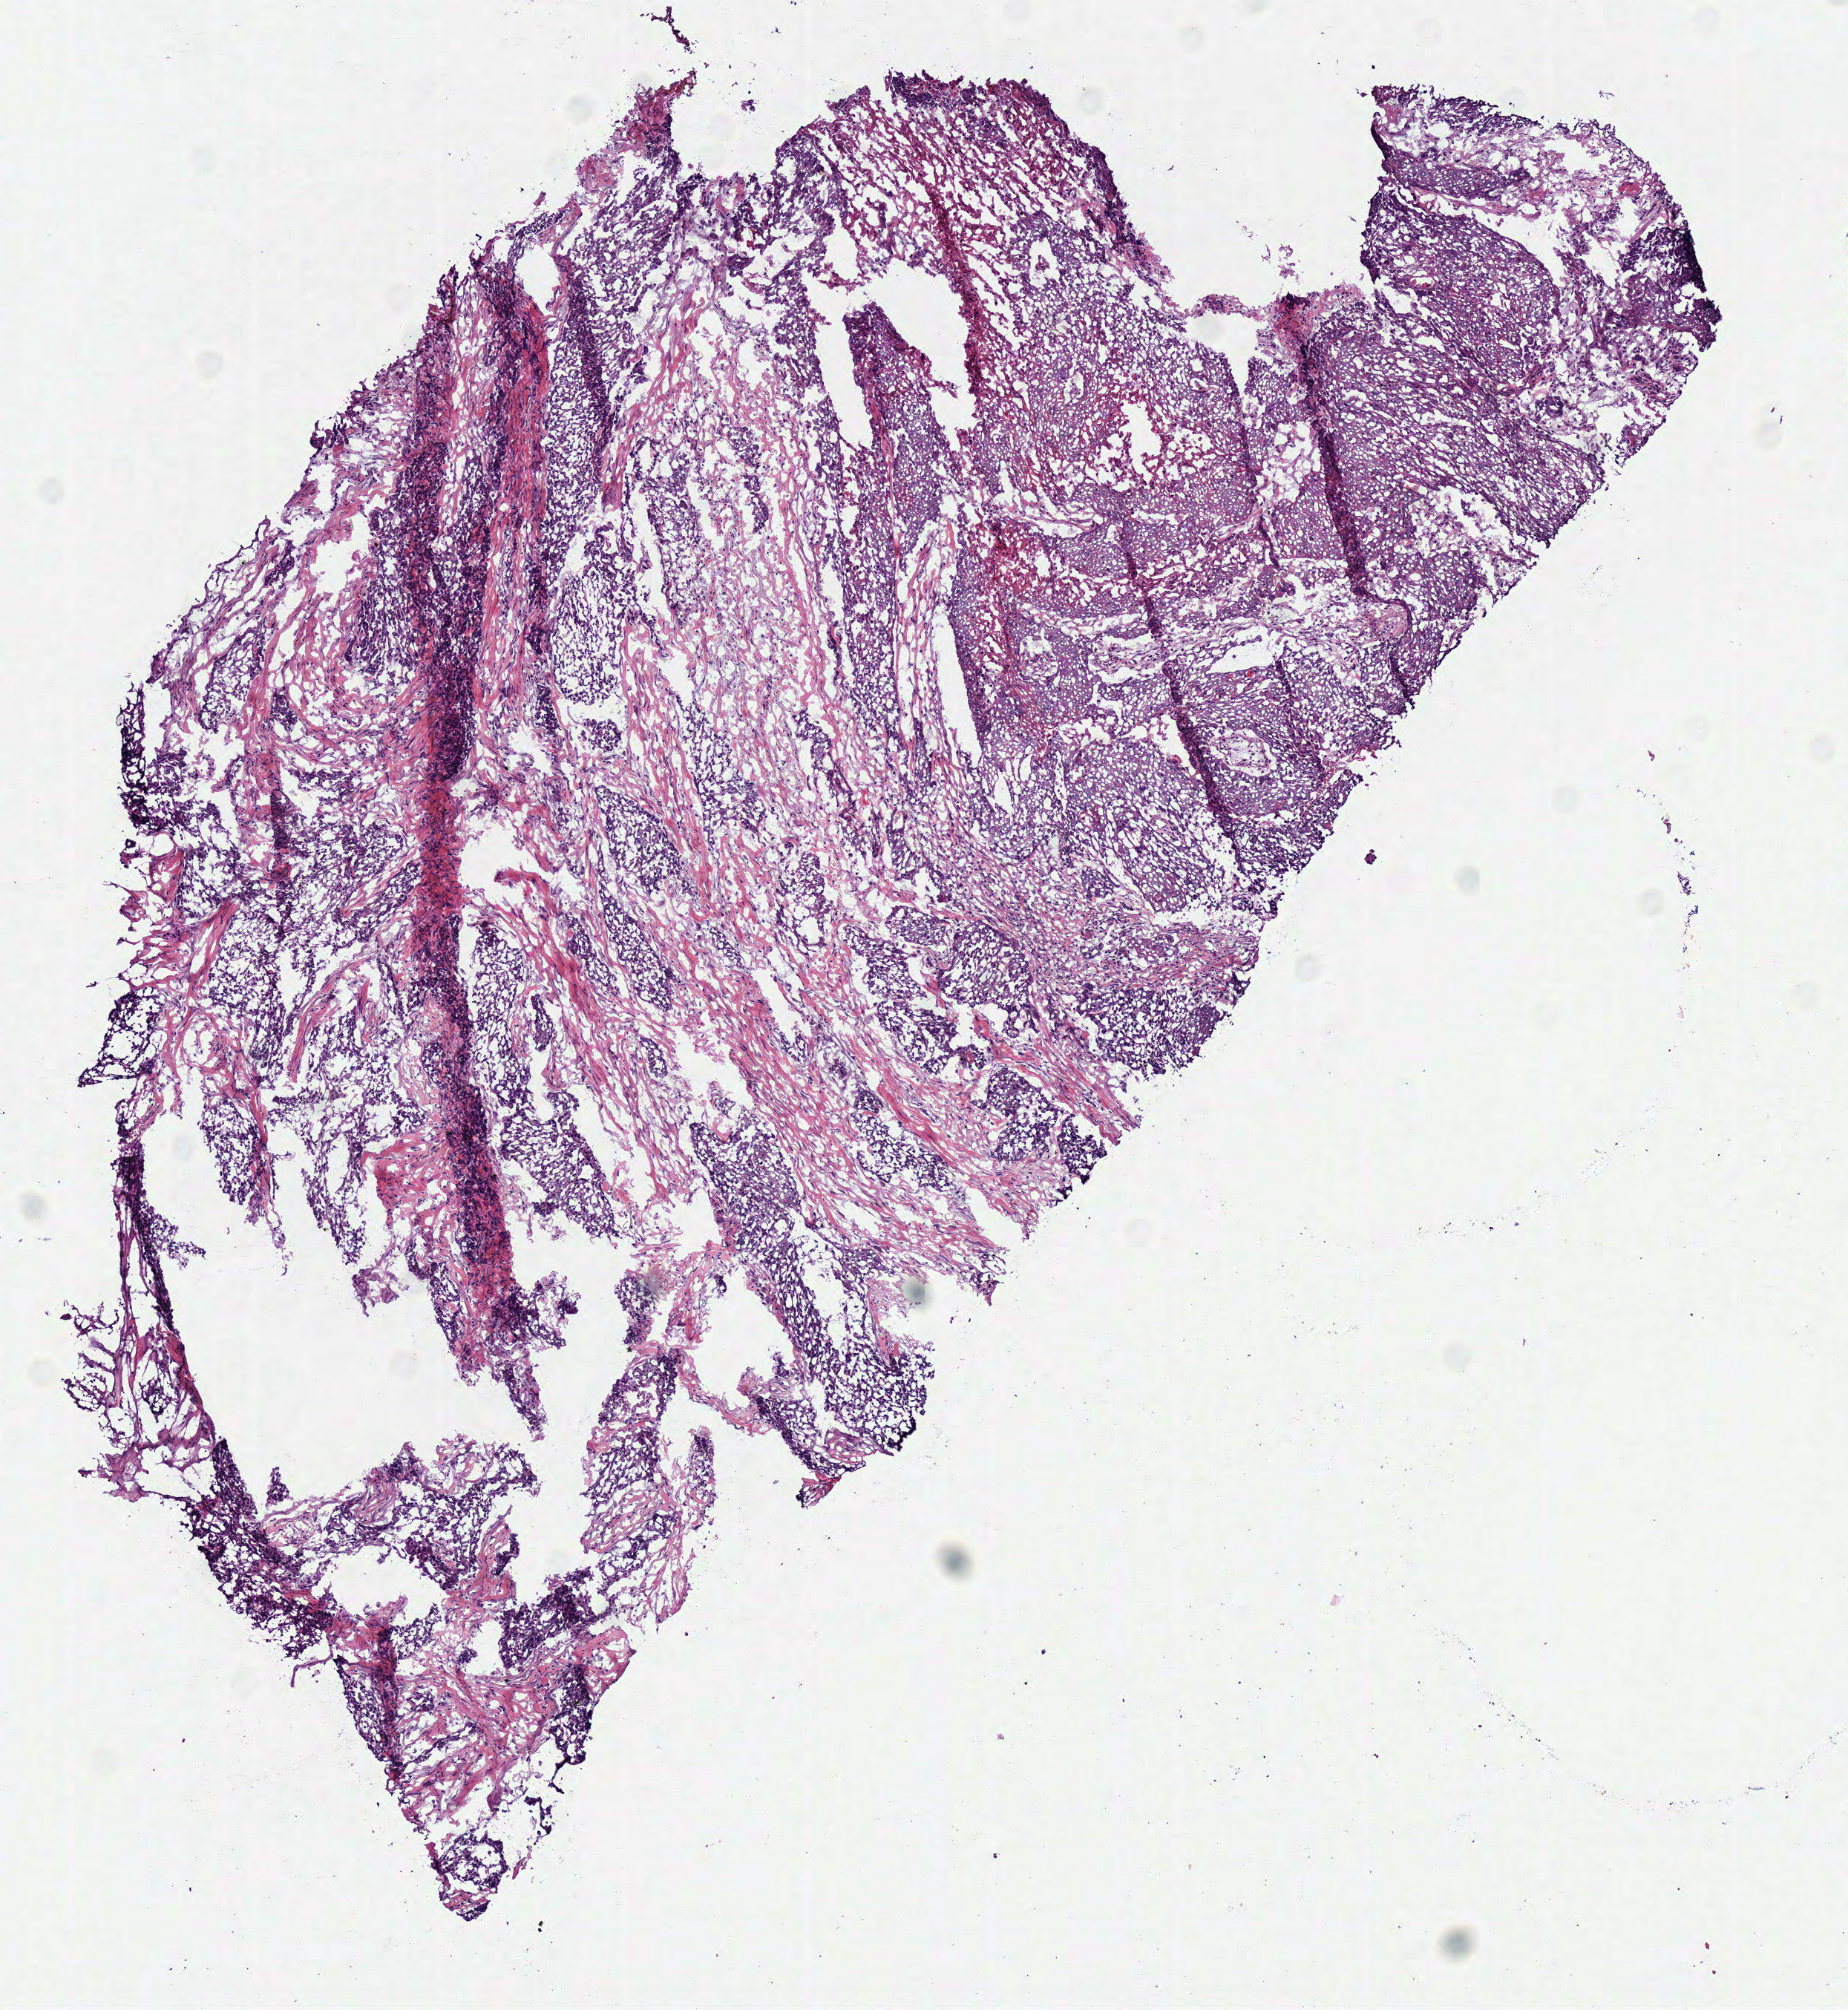
Digitized Hematoxylin and eosin (H&E) stained tissue section (whole slide), whole scanned area (about 4.9 x 5.3 mm) shown as a low-resolution overview, frozen section from the top of the tissue portion, sample: primary tumour, head and neck. Female, age 71 years at initial diagnosis.
Pathologic diagnosis: Squamous cell carcinoma, NOS (overlapping lesion of lip, oral cavity and pharynx).